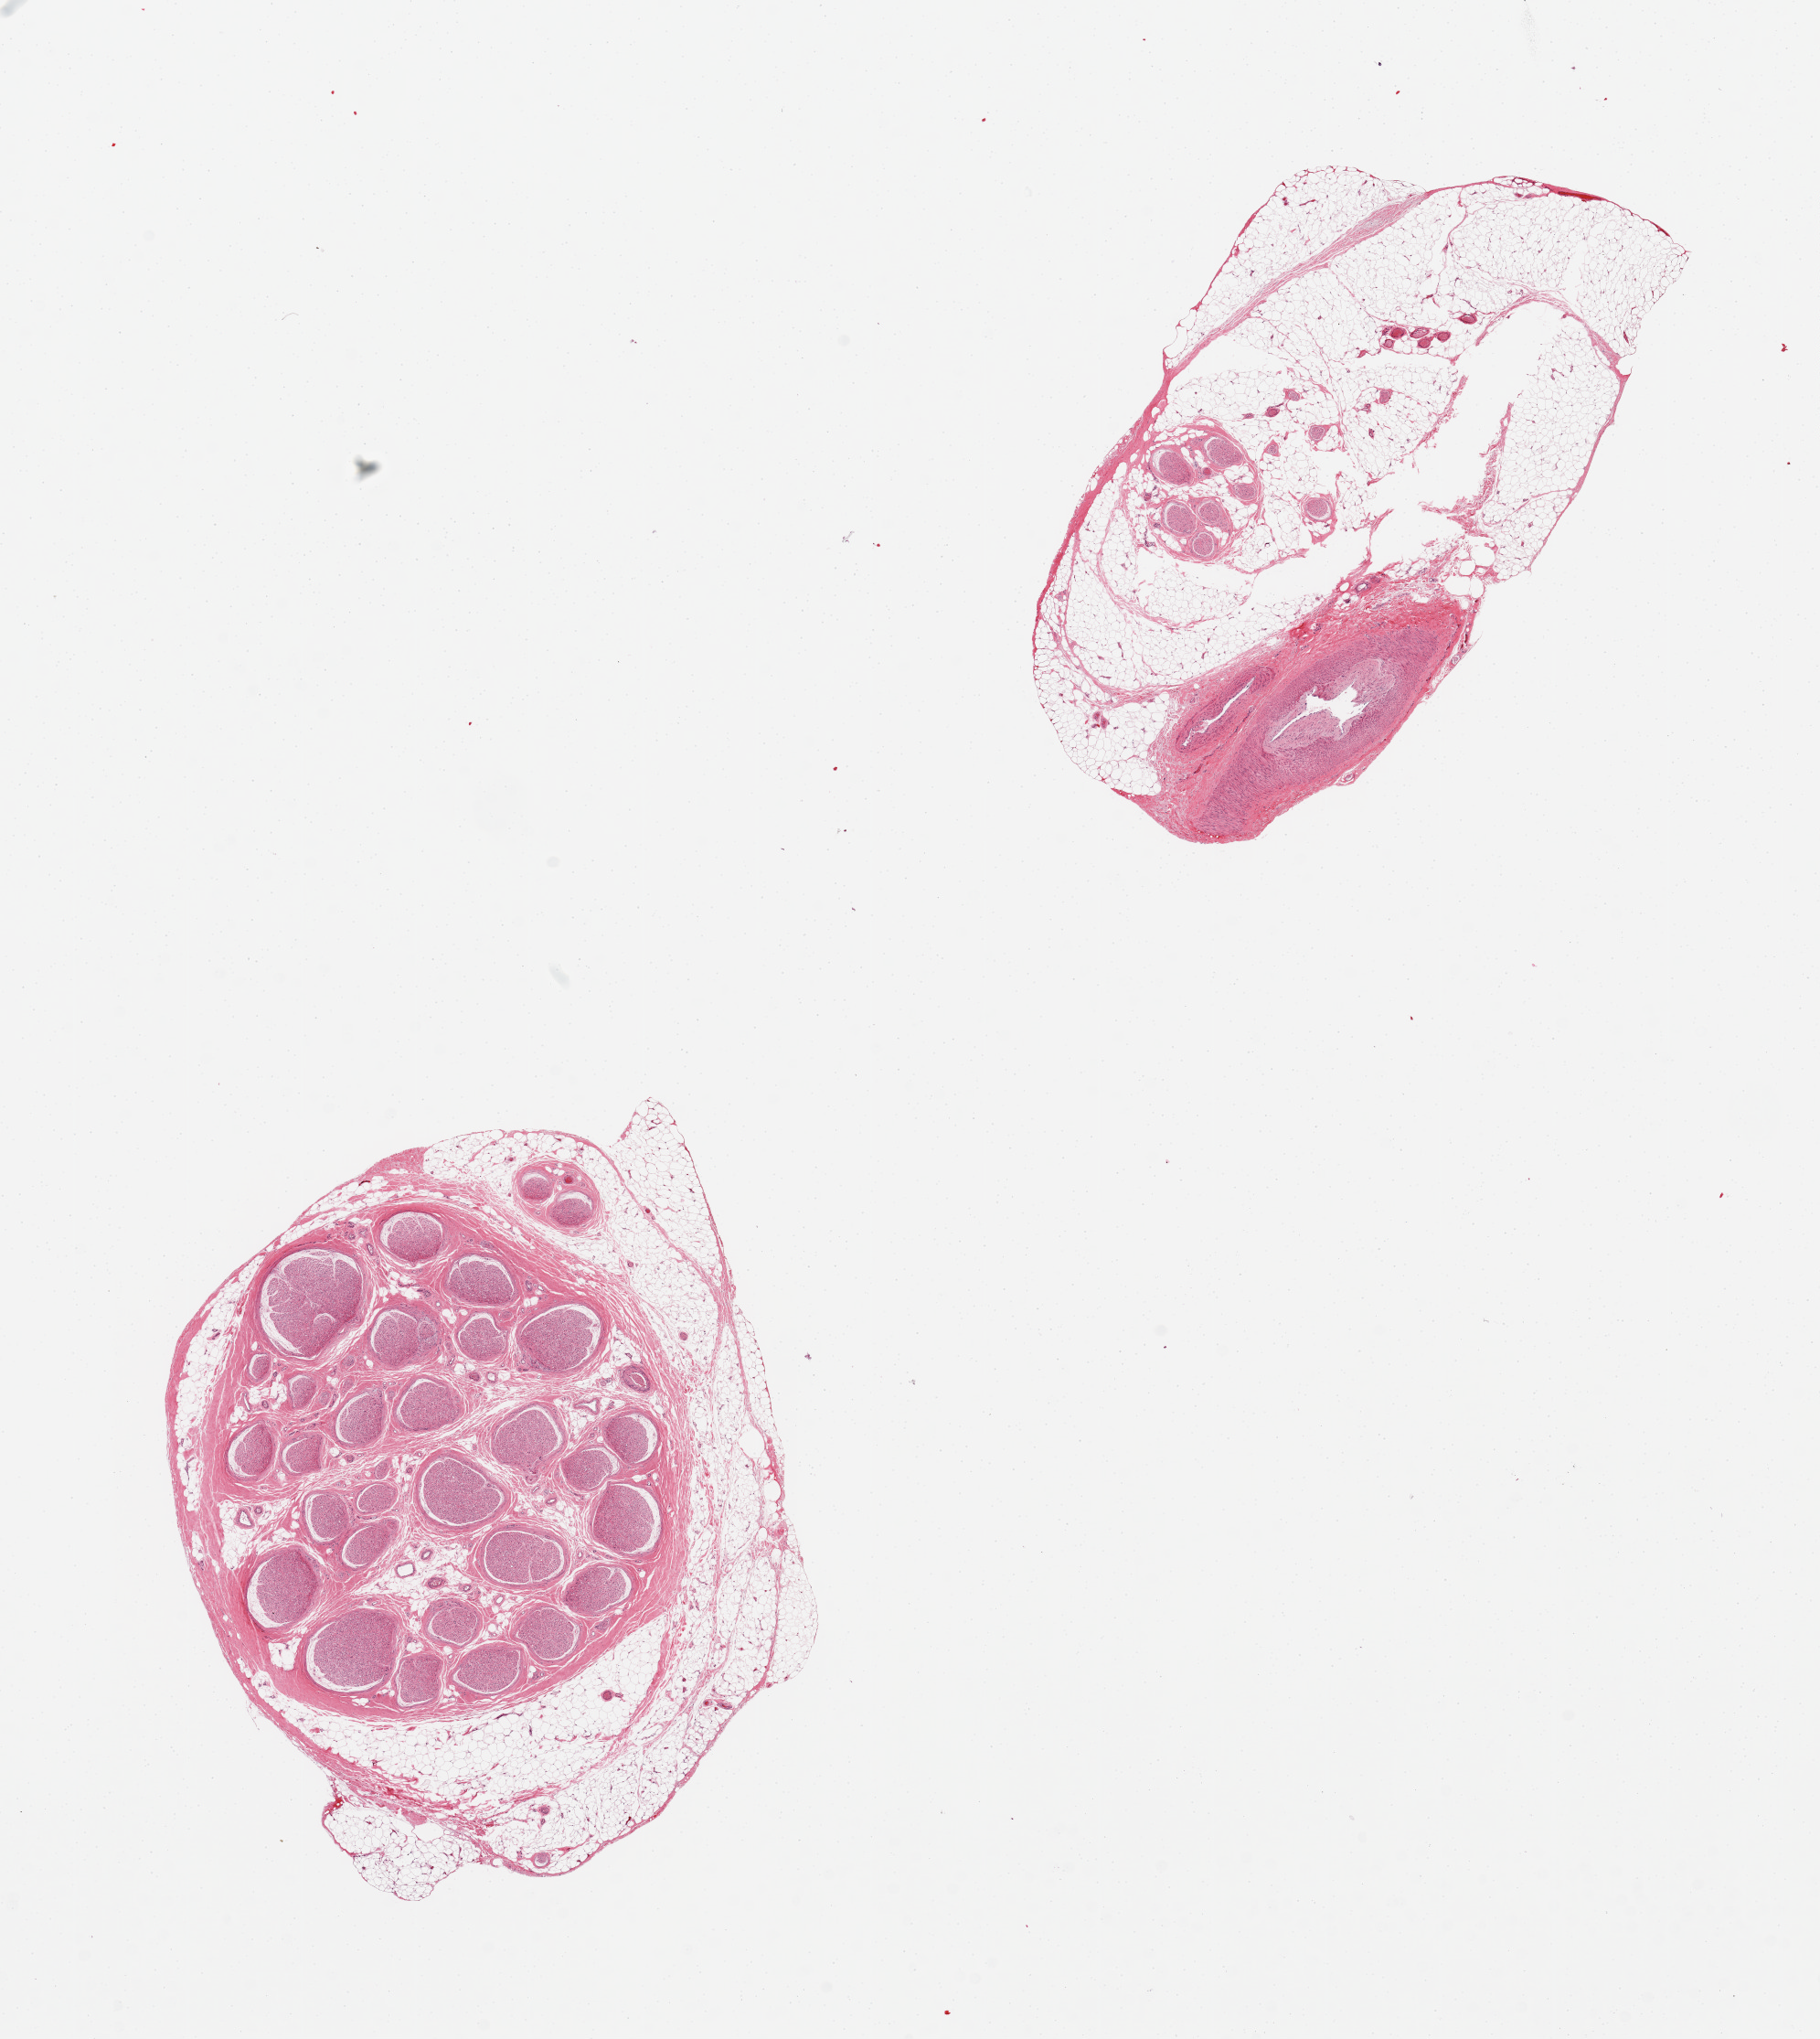
Digitized hematoxylin and eosin (H&E)-stained section, brightfield, low-resolution overview of the scanned area, about 15.8 x 17.6 mm (acquisition: 20x scan), PAXgene-fixed, paraffin-embedded tissue, sampled site (target tissue): tibial nerve, tissue donor sample.
Pathologist's review note for this sample: 2 pieces, one piece includes rim of attached fat (~40%), second piece is only ~5% nerve (predominantly fat and vessels), central hole.